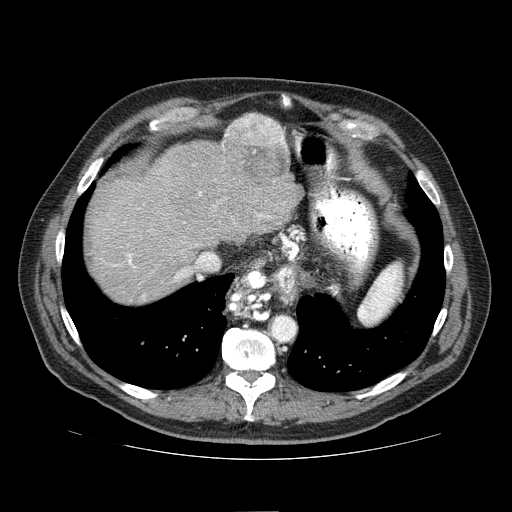
Contrast-enhanced abdominal CT (liver protocol), one axial slice; slice 61 of 81 in the series (ordered by position); reconstruction kernel STANDARD; 100 kVp; one of 2 acquisitions stored at this slice position; soft-tissue window (W 400 / L 40 HU); 2.5 mm slice thickness; 512 × 512 image matrix. Case-level facts recorded for this patient, not image findings: diagnosis: hepatocellular carcinoma (patient treated with transarterial chemoembolisation; whether this scan precedes or follows treatment is not stated here); TNM stage (as recorded): Stage-IIIA.
Outlined on this slice (semi-automatically segmented with operator editing):
- abdominal aorta: bounding box <272,317,295,340> (left, top, right, bottom; pixels)
- liver parenchyma outside the tumour (the mass and vessels are separate outlines, so this box may not span the whole liver): <90,114,300,304>
- mass: <221,113,290,184>
- liver vessels: <112,191,271,280>